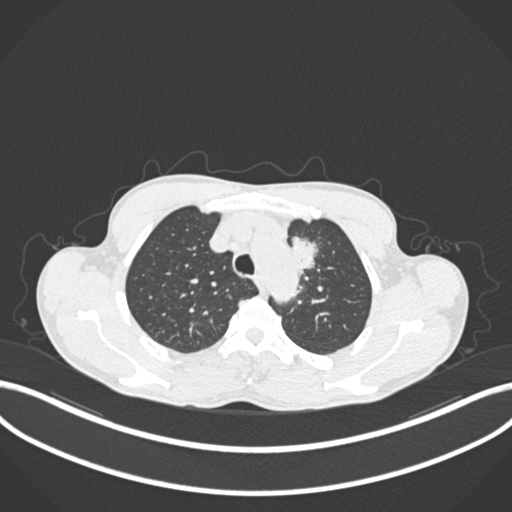
Chest CT, one axial slice. Reconstruction kernel B30f. Lung window (W 1500 / L -600 HU). 1 mm slice thickness. 512 × 512 image matrix, field of view 400 × 400 mm. Male patient, age 58 years. Case-level facts recorded for this patient, not image findings: clinical TNM (as recorded): T1c N1 M0.
Structures marked on this image (bounding box drawn by a radiologist):
- lung tumour (recorded histology: adenocarcinoma): bounding box [x1, y1, x2, y2] px = [289, 233, 319, 278]